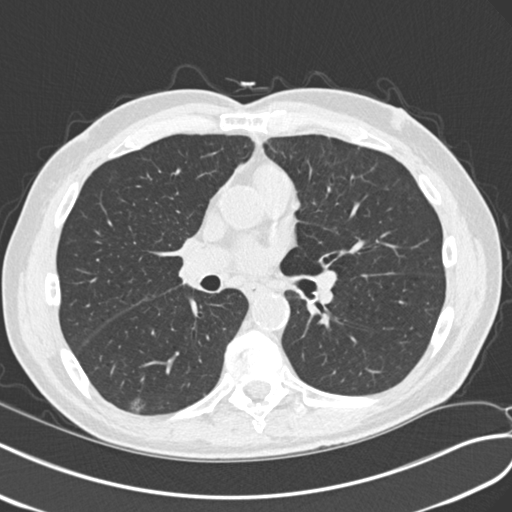
Low-dose screening chest CT, axial slice; second annual screen; lung window (W 1500 / L -600 HU); 2 mm slice thickness; standard (soft-tissue) reconstruction kernel (B30f); 120 kVp. Male, age 68 years at enrolment. Current smoker at enrolment.
- Expert reader's lesion annotation, bounding box <108,383,158,421> (left, top, right, bottom; pixels).
- The screening reader recorded 4 non-calcified nodules or masses ≥4 mm on this exam; which of them this box marks is not recorded.
- Participant outcome: lung cancer diagnosed 653 days after this screen — non-small cell carcinoma, right lower lobe, poorly differentiated (G3), stage IA (AJCC 6th edition), 23 mm at pathology.